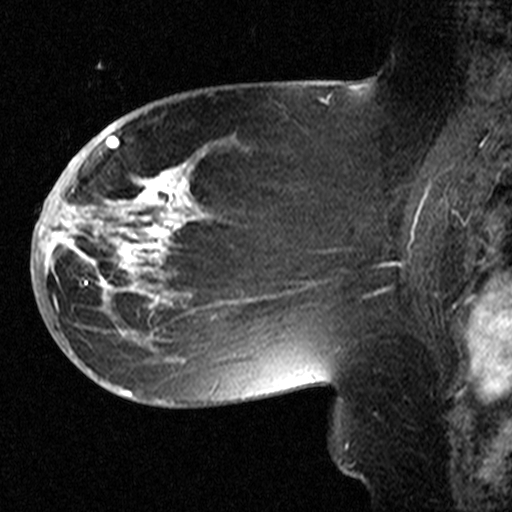
Breast MRI (dynamic contrast-enhanced), one sagittal slice. Slice 21 of 44 in the series (ordered by position). Dynamic contrast-enhanced study with each time point stored as its own series, time point 2 of 3 at this slice position (early post-contrast, ordered by acquisition time). 1.5 T. TE 4.5 ms, TR 11 ms. 512 × 512 image matrix, field of view 200 × 200 mm. Patient: female, 53 years. Case-level facts recorded for this patient, not image findings: setting: breast cancer imaged before/during neoadjuvant chemotherapy; receptor status: HR-positive, HER2-negative.
Outlined on this slice (semi-automatically segmented with operator editing):
- analysis volume of interest (the breast-tissue region the enhancement analysis was run in; not a lesion): bounding box (x1, y1, x2, y2) in pixels: (58, 154, 311, 367)
- tumour enhancement mask (voxels above the 90 % enhancement threshold inside the analysis volume of interest): (58, 166, 203, 309)